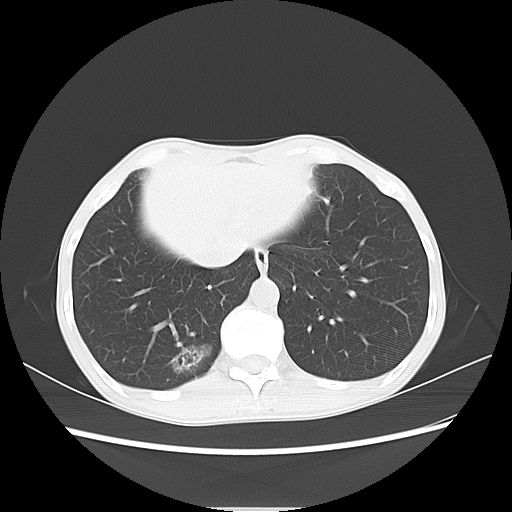
Chest CT, one axial slice. Slice 18 of 69 in the series (ordered by position). Lung window (W 1500 / L -600 HU). 512 × 512 image matrix. Female patient, age 51 years. Case-level facts recorded for this patient, not image findings: clinical TNM (as recorded): T1c N0 M0; histopathological grade: G2-3.
Annotated regions visible in this slice (bounding box drawn by a radiologist):
- lung tumour (recorded histology: adenocarcinoma): bounding box <171,338,218,383> (left, top, right, bottom; pixels)